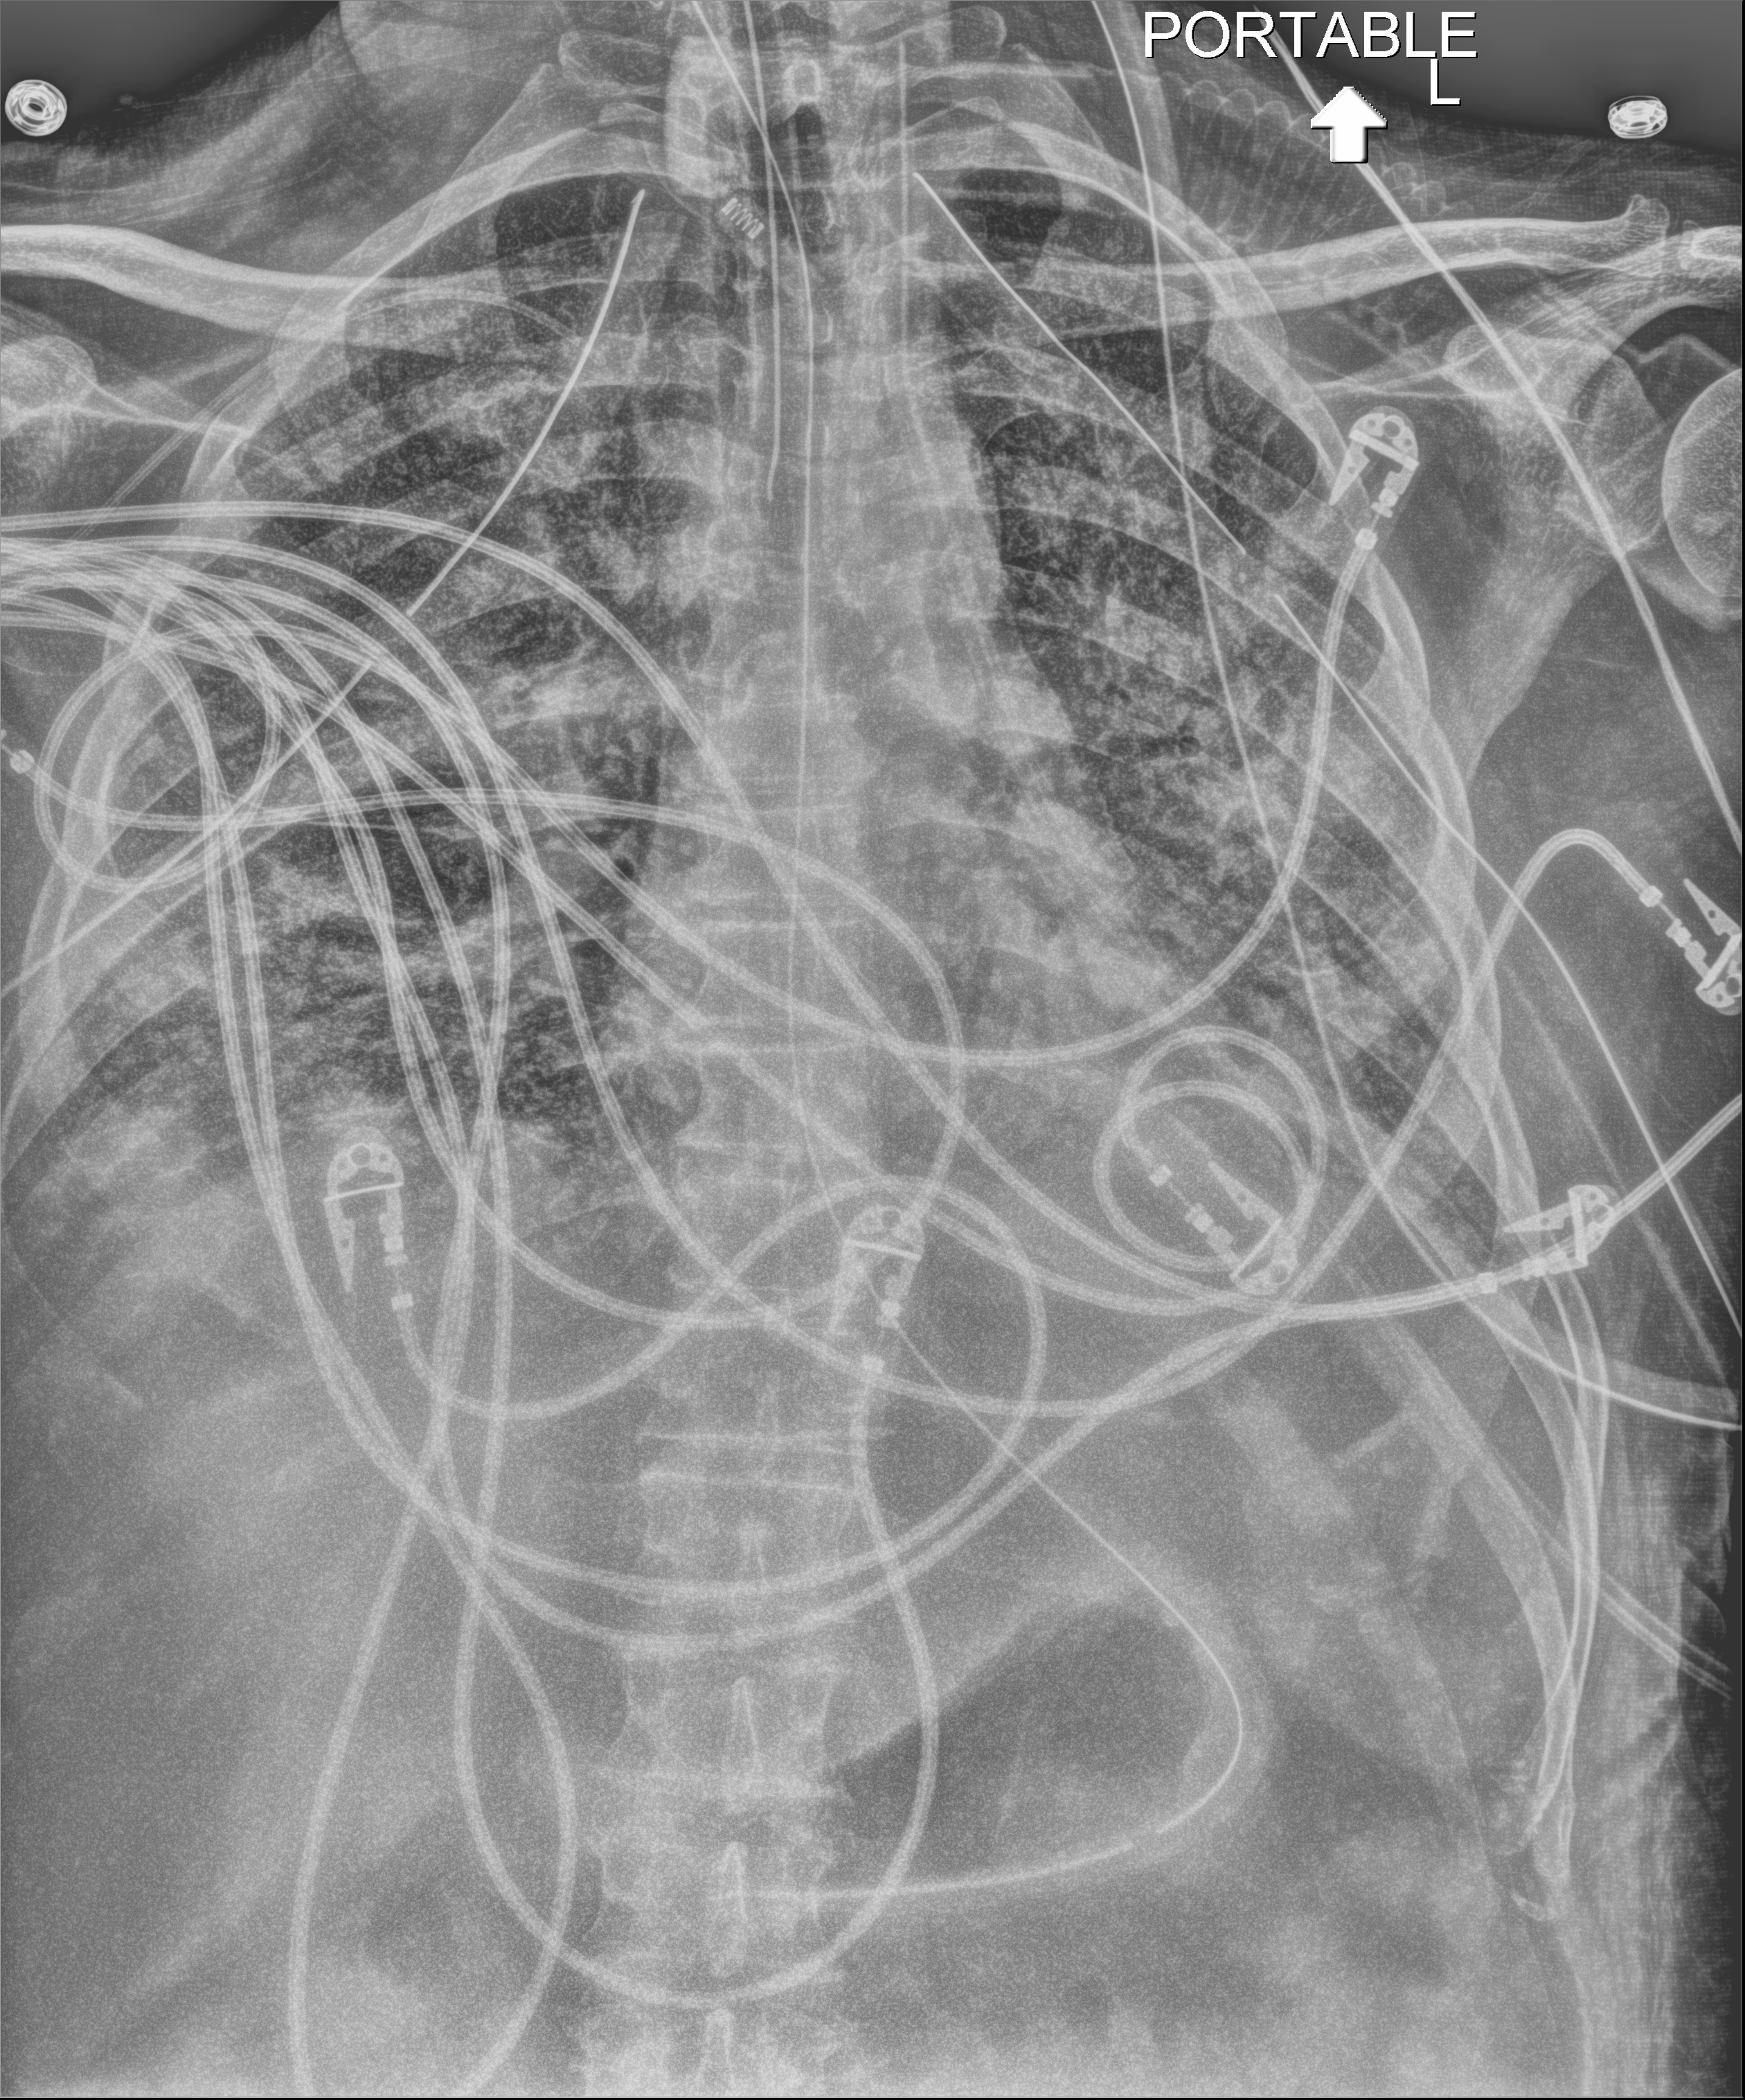
Portable chest radiograph, anteroposterior (AP) projection. Male patient hospitalised with COVID-19, age 18–59 years.
From the hospital-stay record, not from the radiograph (when in the stay this image was taken is not recorded):
- mechanically ventilated during this hospital stay: yes
- length of hospital stay: 83 days